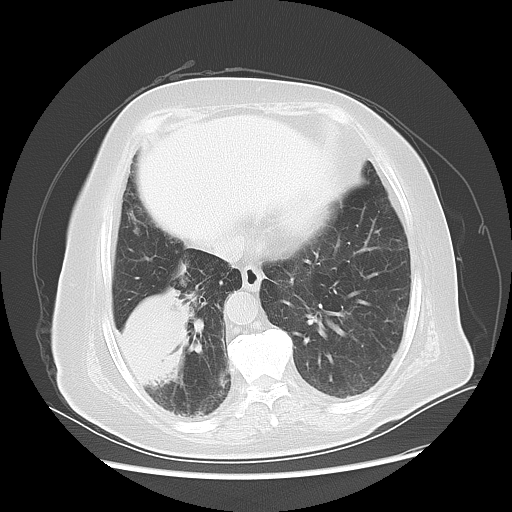
Chest CT, one axial slice. Slice 18 of 56 in the series (ordered by position). Reconstruction kernel LUNG. 120 kVp. Lung window (W 1500 / L -600 HU). 5 mm slice thickness. 512 × 512 image matrix. Female patient, age 73 years. Case-level facts recorded for this patient, not image findings: clinical TNM (as recorded): T3 N0 M0.
Outlined on this slice (rectangle marked by the reading radiologist):
- lung tumour (recorded histology: adenocarcinoma): bounding box (x1, y1, x2, y2) in pixels: (115, 286, 196, 392)